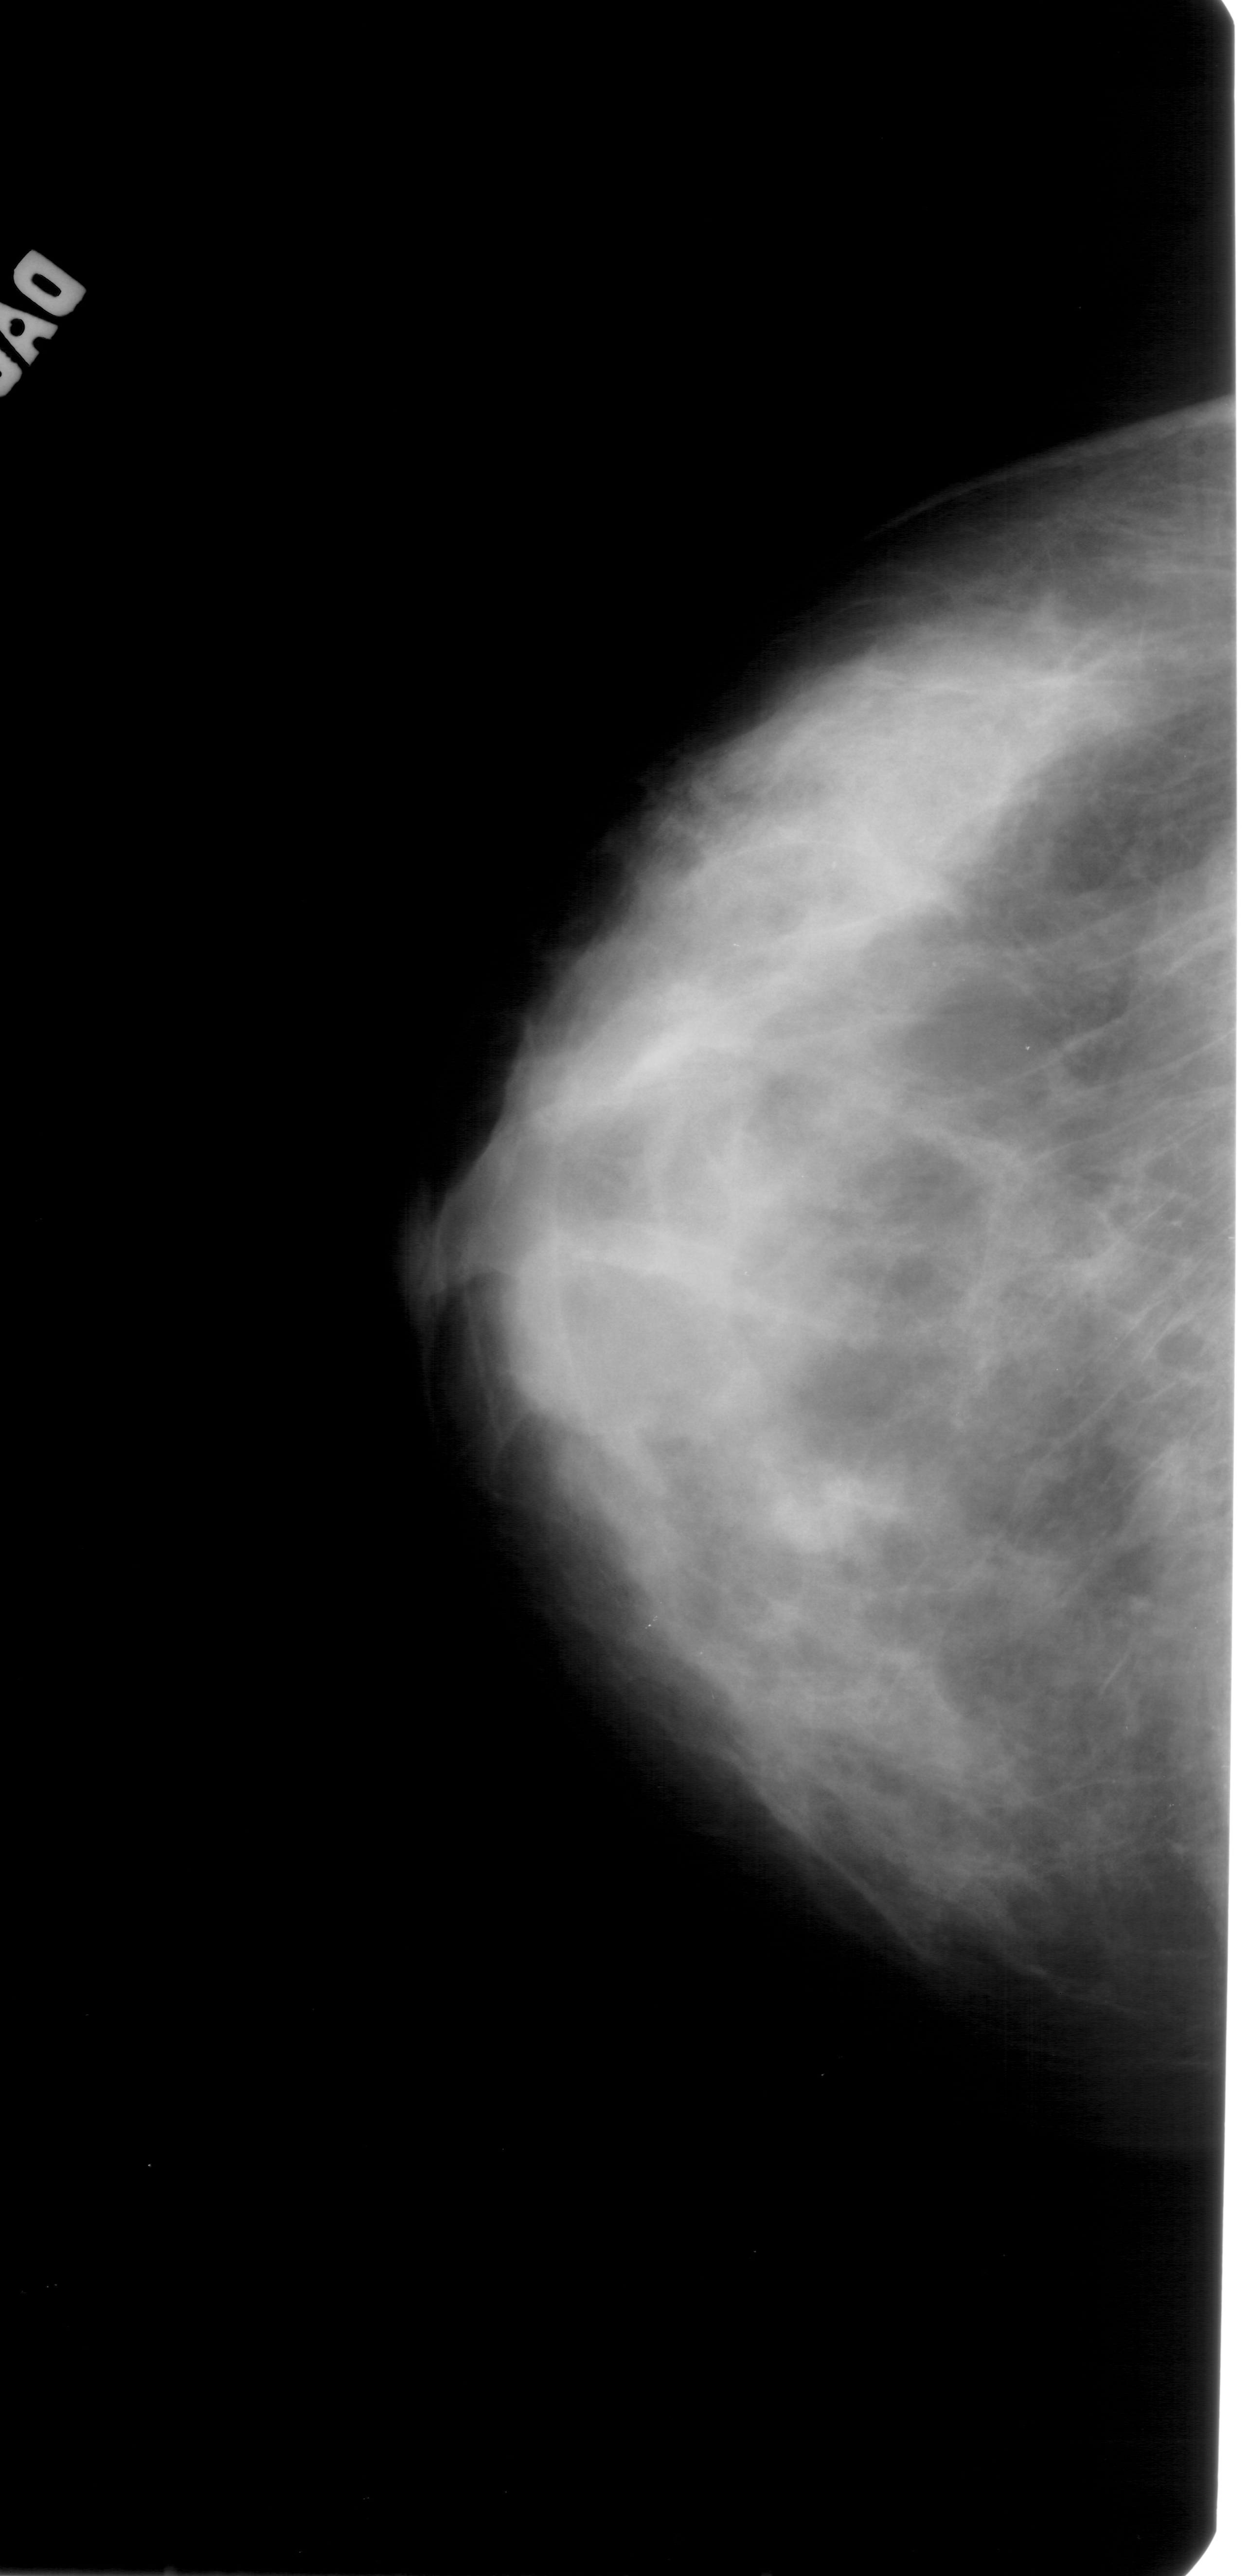
Digitized screen-film mammogram, left breast, craniocaudal (CC) view, breast composition: extremely dense (BI-RADS density category 4 of 4).
Abnormality record for this image: calcifications, morphology pleomorphic, distribution segmental; BI-RADS assessment category 4; pathology result (as recorded, not read from the image): benign.